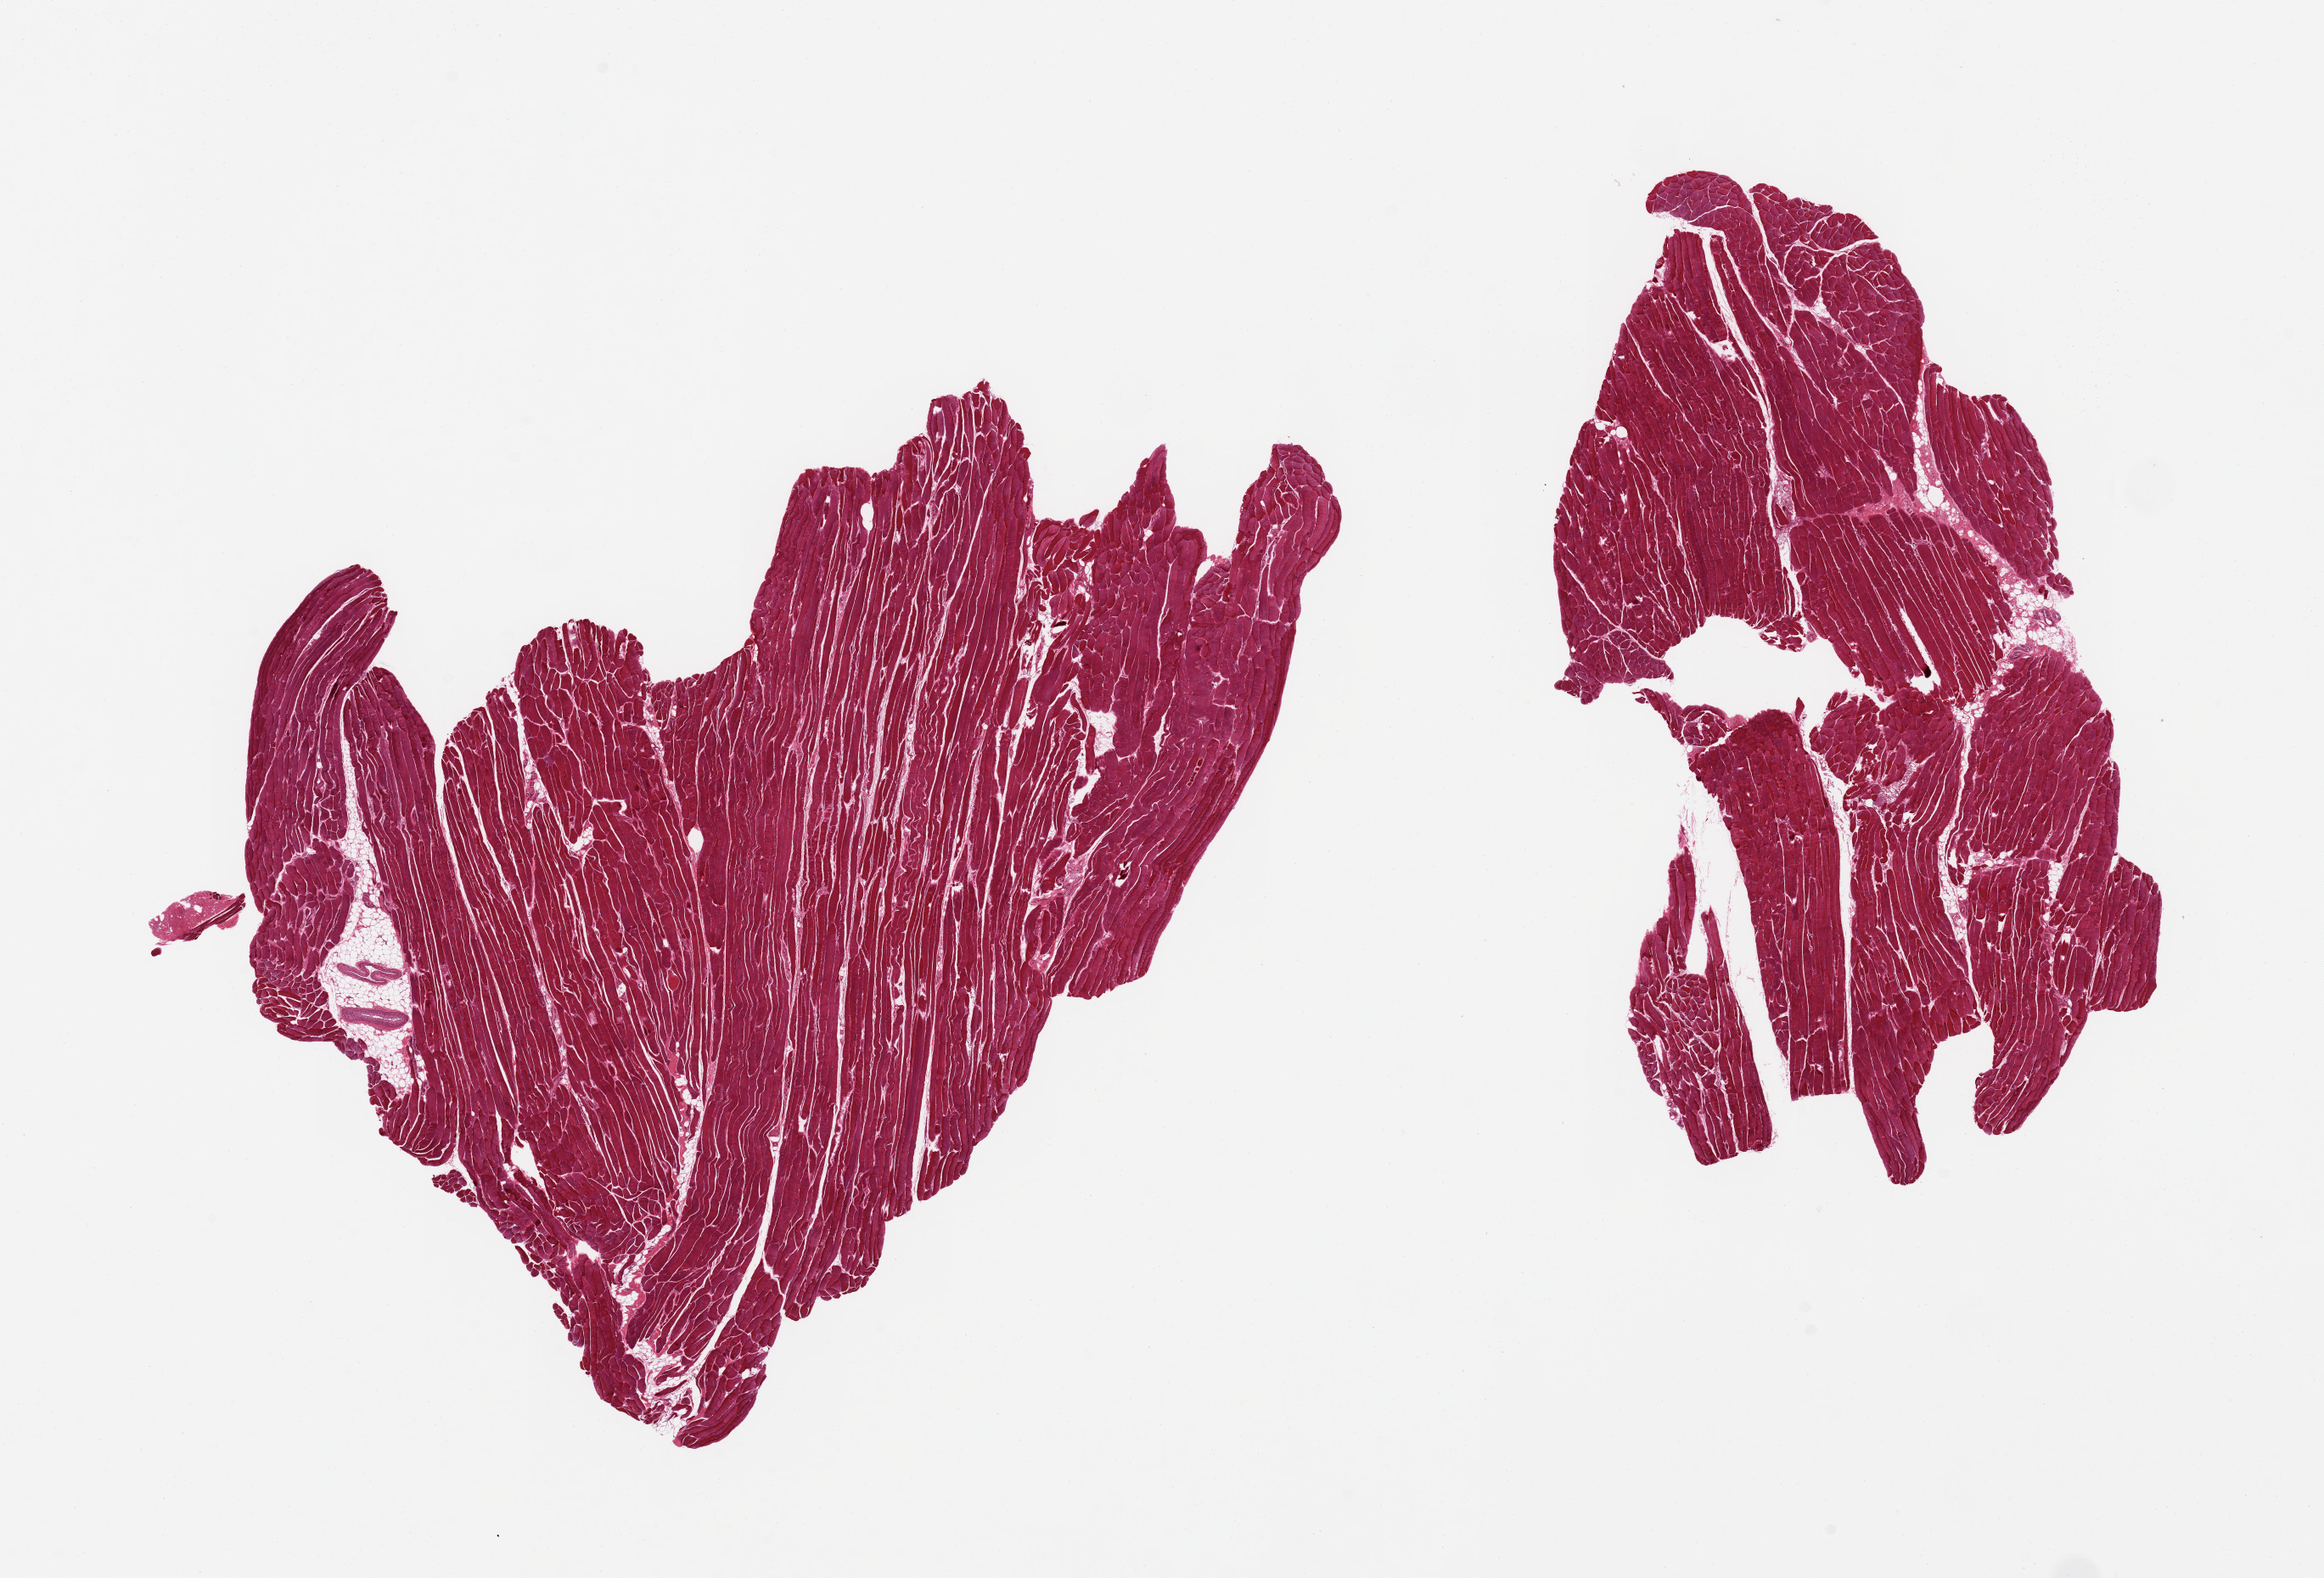
Haematoxylin and eosin whole-slide image, shown as a low-resolution overview of the whole scanned area (about 21.7 x 14.7 mm, from a 20x scan); PAXgene-fixed paraffin-embedded (PFPE) section; section of skeletal muscle (target tissue); tissue donor sample. Male donor.
Reviewer comment on this tissue sample: 2 pieces, ~10% interstitial fat.